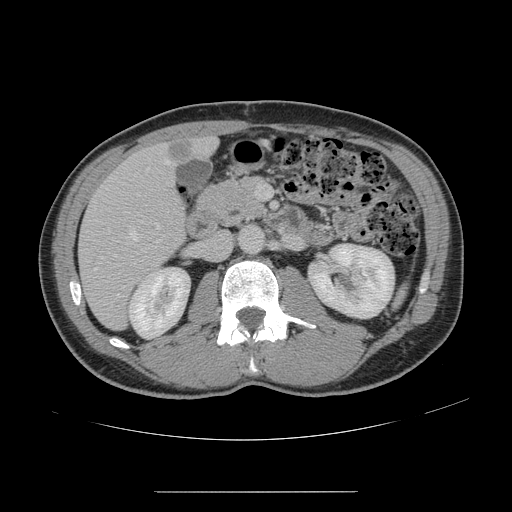
Contrast-enhanced abdominal CT, one axial slice. 120 kVp. Intravenous contrast given. Soft-tissue window (W 400 / L 40 HU). 2.5 mm slice thickness. 512 × 512 image matrix, field of view 401 × 401 mm. Male patient, age 53 years. From the clinical record (not read from this slice): diagnosis: colorectal cancer liver metastases, imaged before liver resection; multiple liver metastases: yes; largest metastasis: 2.4 cm; disease in both lobes: no.
Outlined on this slice (outlined manually by an expert reader):
- hepatic veins: bounding box (x1, y1, x2, y2) in pixels: (94, 160, 170, 271)
- liver: (80, 138, 215, 328)
- planned liver remnant (the part of the liver to remain after resection): (198, 138, 215, 155)
- portal vein (with intrahepatic branches): (137, 185, 267, 199)
- liver metastasis: (167, 143, 193, 159)